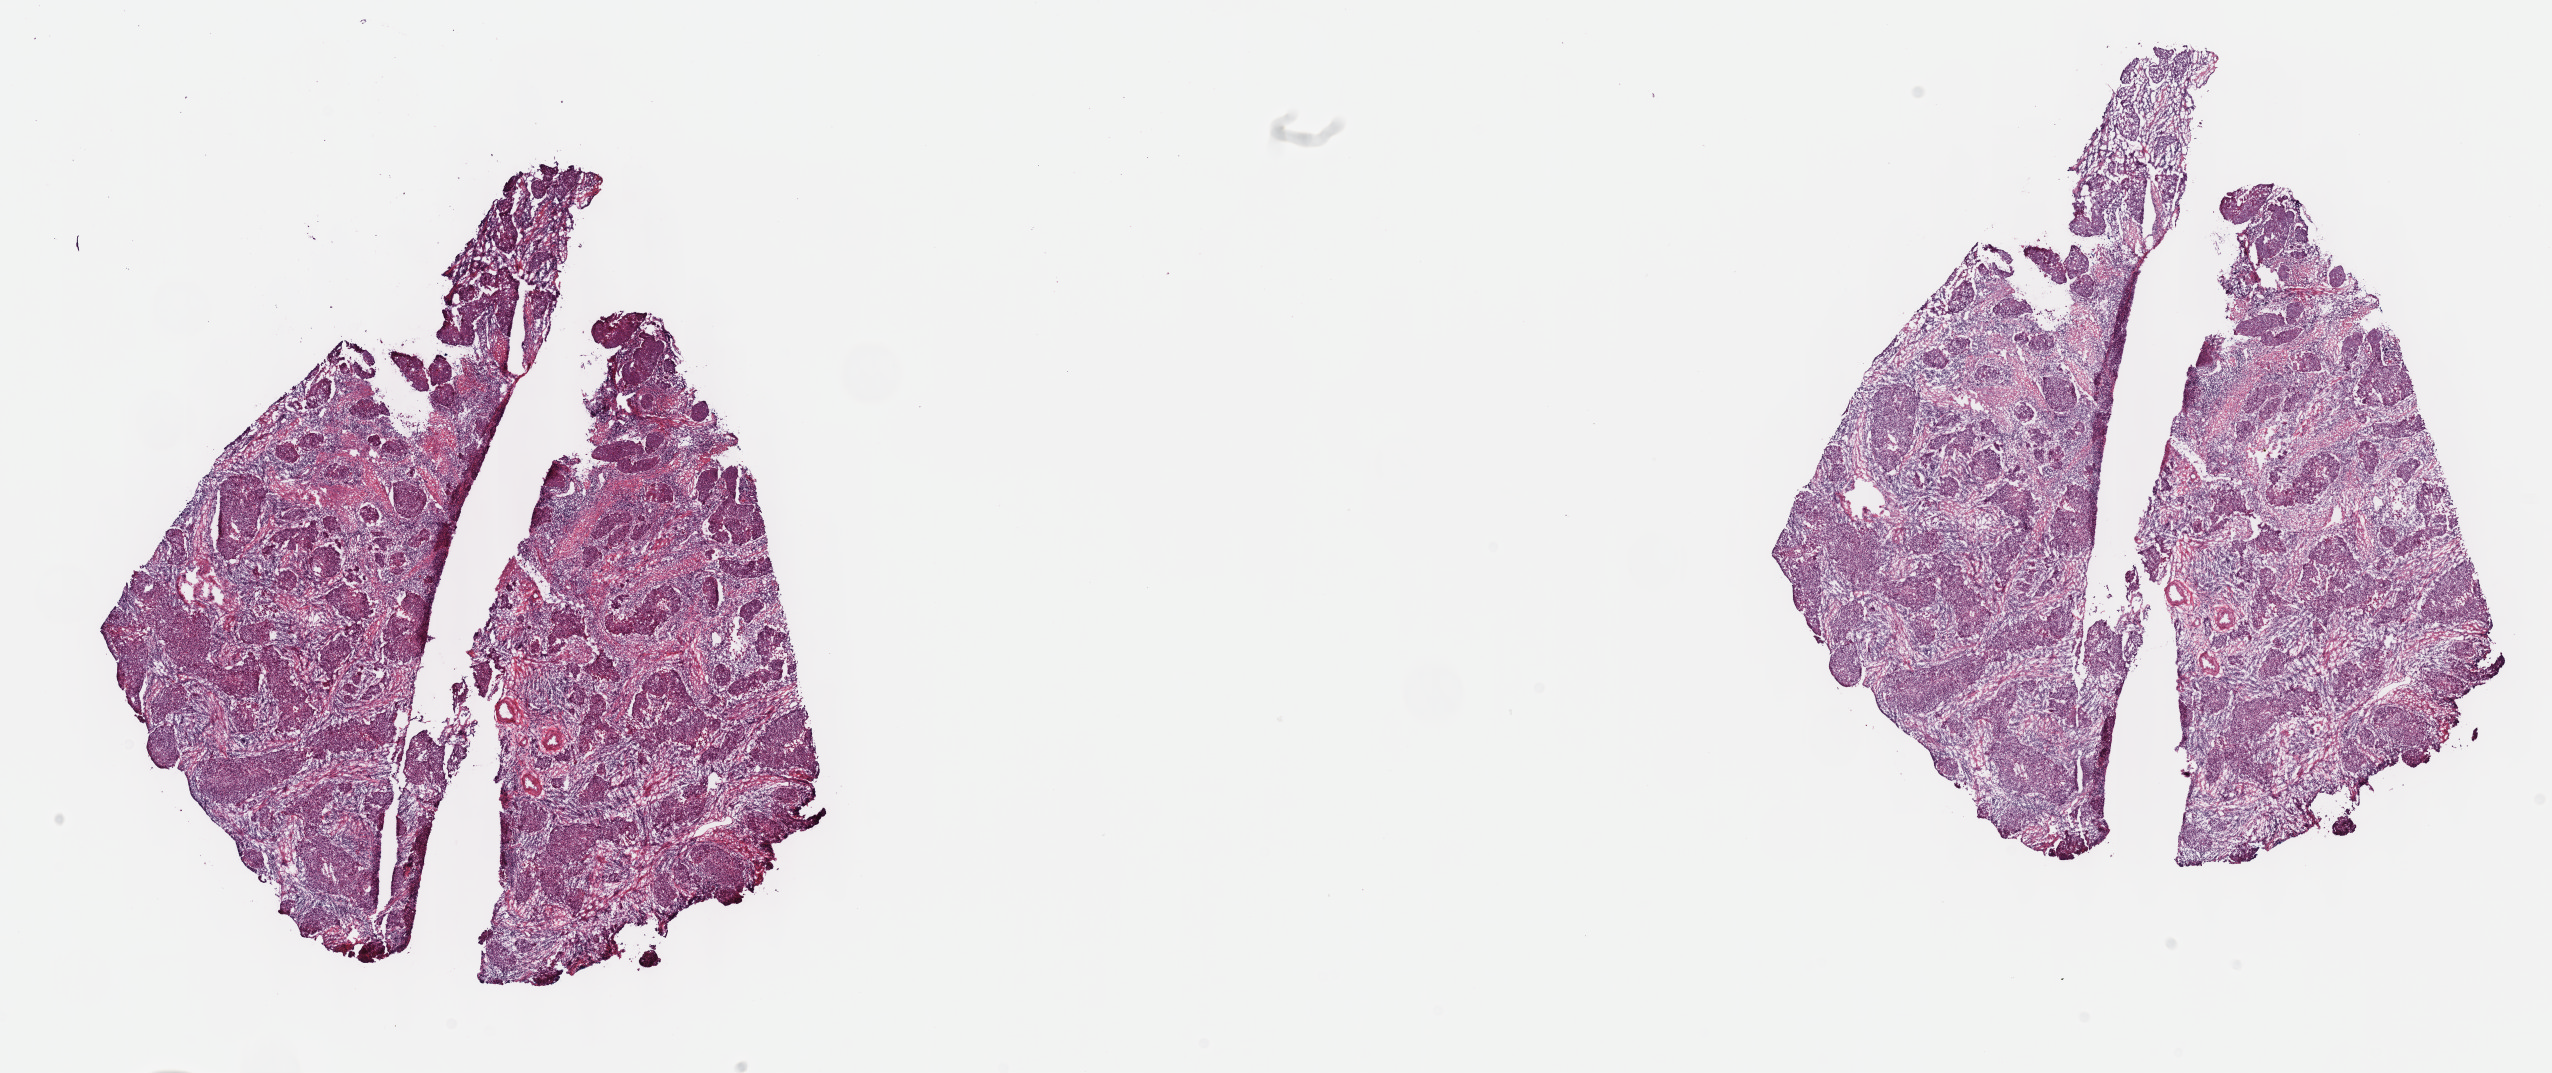
H&E whole-slide image — low-resolution overview of the scanned area, about 20.6 x 8.7 mm (from a 40x scan). Frozen section from the top of the tissue portion. Sample: primary tumour, cervix. Patient: female, age at initial diagnosis 44 years. Histologic grade: G2 (moderately differentiated). Slide review estimates, as recorded: tumour cells 60%, tumour nuclei 60%, normal cells 0%, stromal cells 30%, necrosis 10%. Infiltration values recorded for this section: lymphocyte infiltration 70%, monocyte infiltration 10%, neutrophil infiltration 10%.
Pathologic diagnosis: Squamous cell carcinoma, NOS. FIGO stage: IB1.